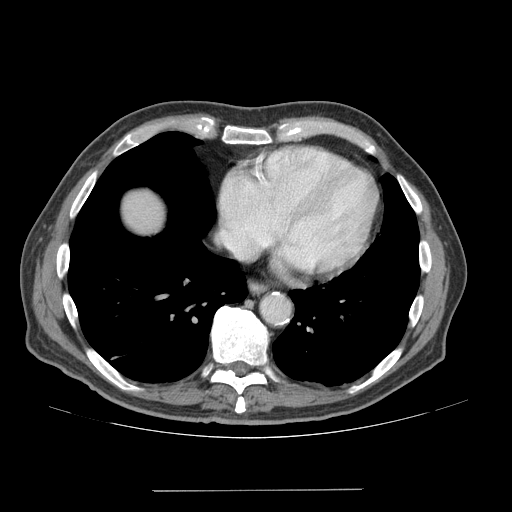
Contrast-enhanced abdominal CT (liver protocol), one axial slice; slice 70 of 77 in the series (ordered by position); reconstruction kernel STANDARD; 140 kVp; soft-tissue window (W 400 / L 40 HU); 2.5 mm slice thickness; 512 × 512 image matrix, field of view 400 × 400 mm. From the clinical record (not read from this slice): diagnosis: hepatocellular carcinoma (patient treated with transarterial chemoembolisation; whether this scan precedes or follows treatment is not stated here); TNM stage (as recorded): Stage-IVA; Child-Pugh class: A; tumour differentiation: well differentiated; tumour nodularity: uninodular.
Annotated regions visible in this slice (semi-automatic segmentation, software-assisted and operator-edited):
- liver parenchyma outside the tumour (the mass and vessels are separate outlines, so this box may not span the whole liver): box from (x=122, y=190) to (x=164, y=234) px